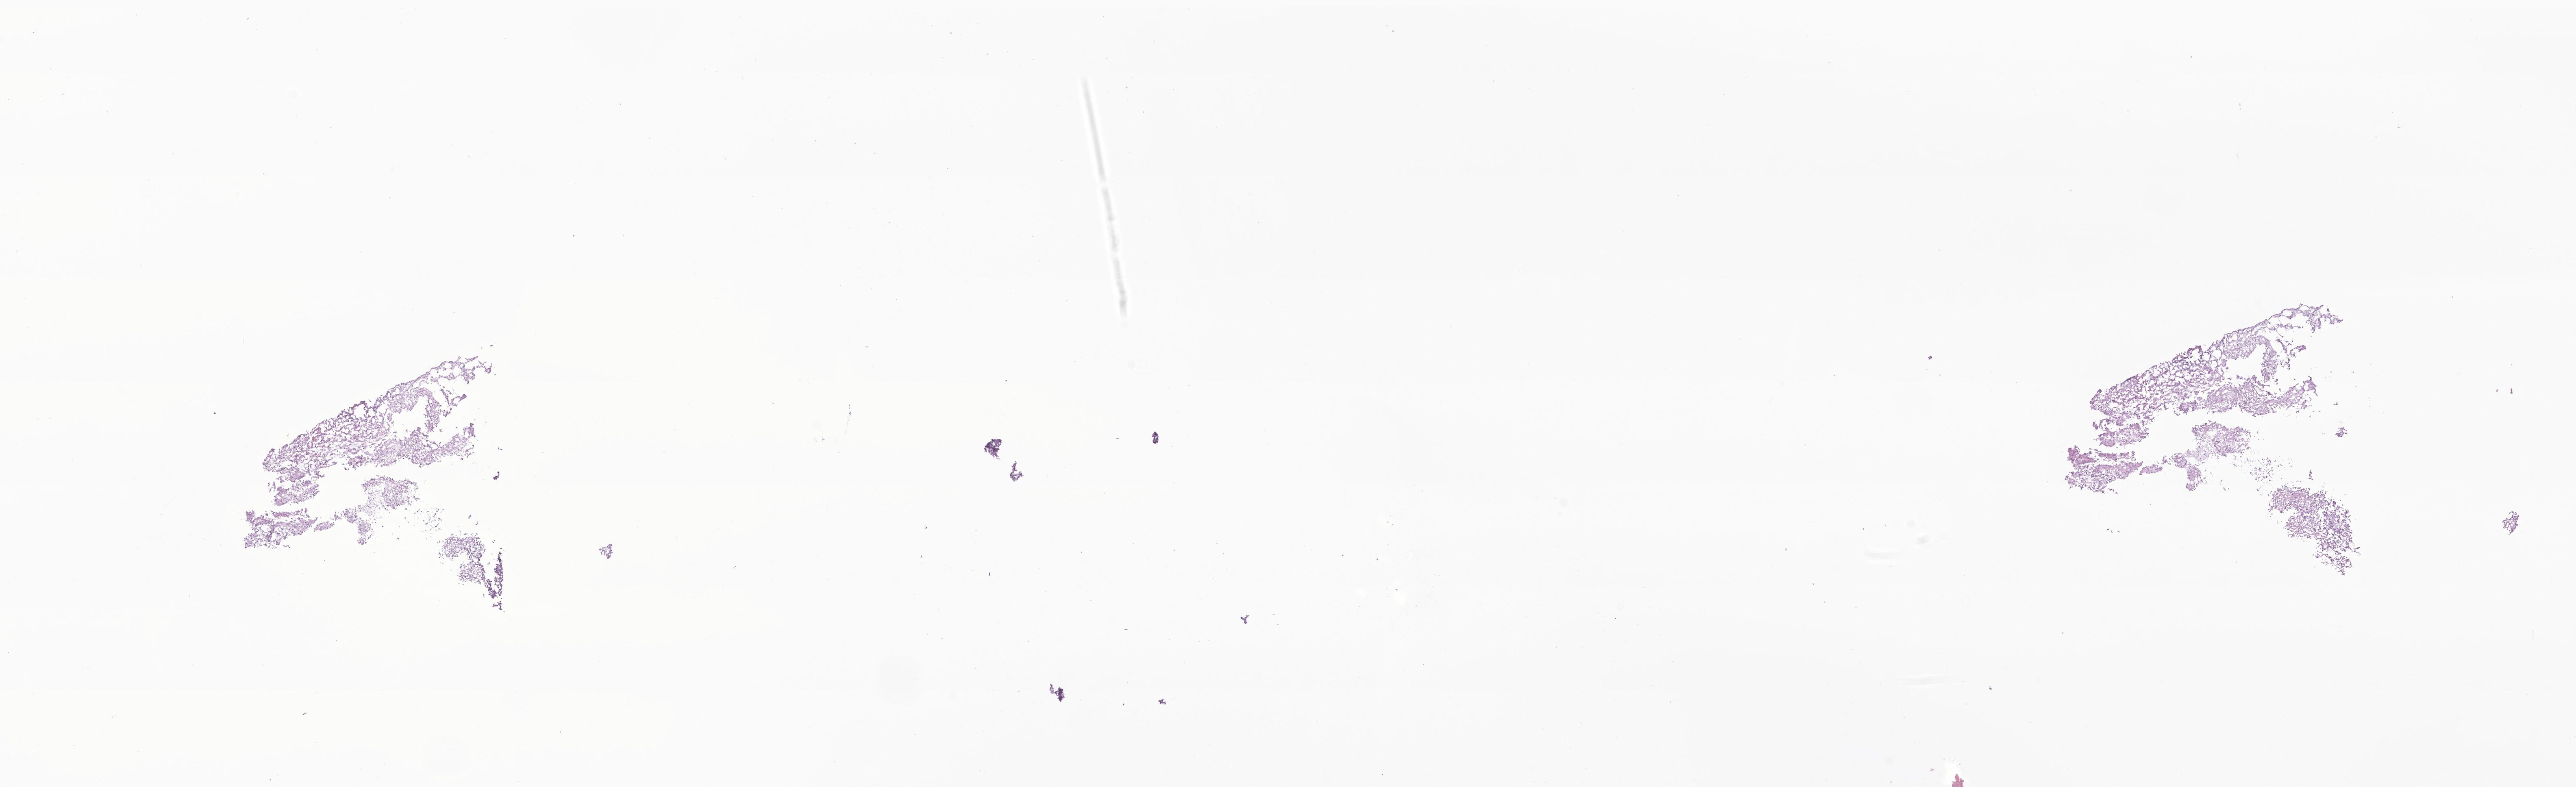
Whole-slide image, H&E stain of tumor tissue from the frontal lobe, low-resolution overview of the scanned area, about 26.7 x 8.2 mm; frozen section (OCT-embedded). Patient: female, age 344 days.
Diagnosis: Desmoplastic infantile astrocytoma.